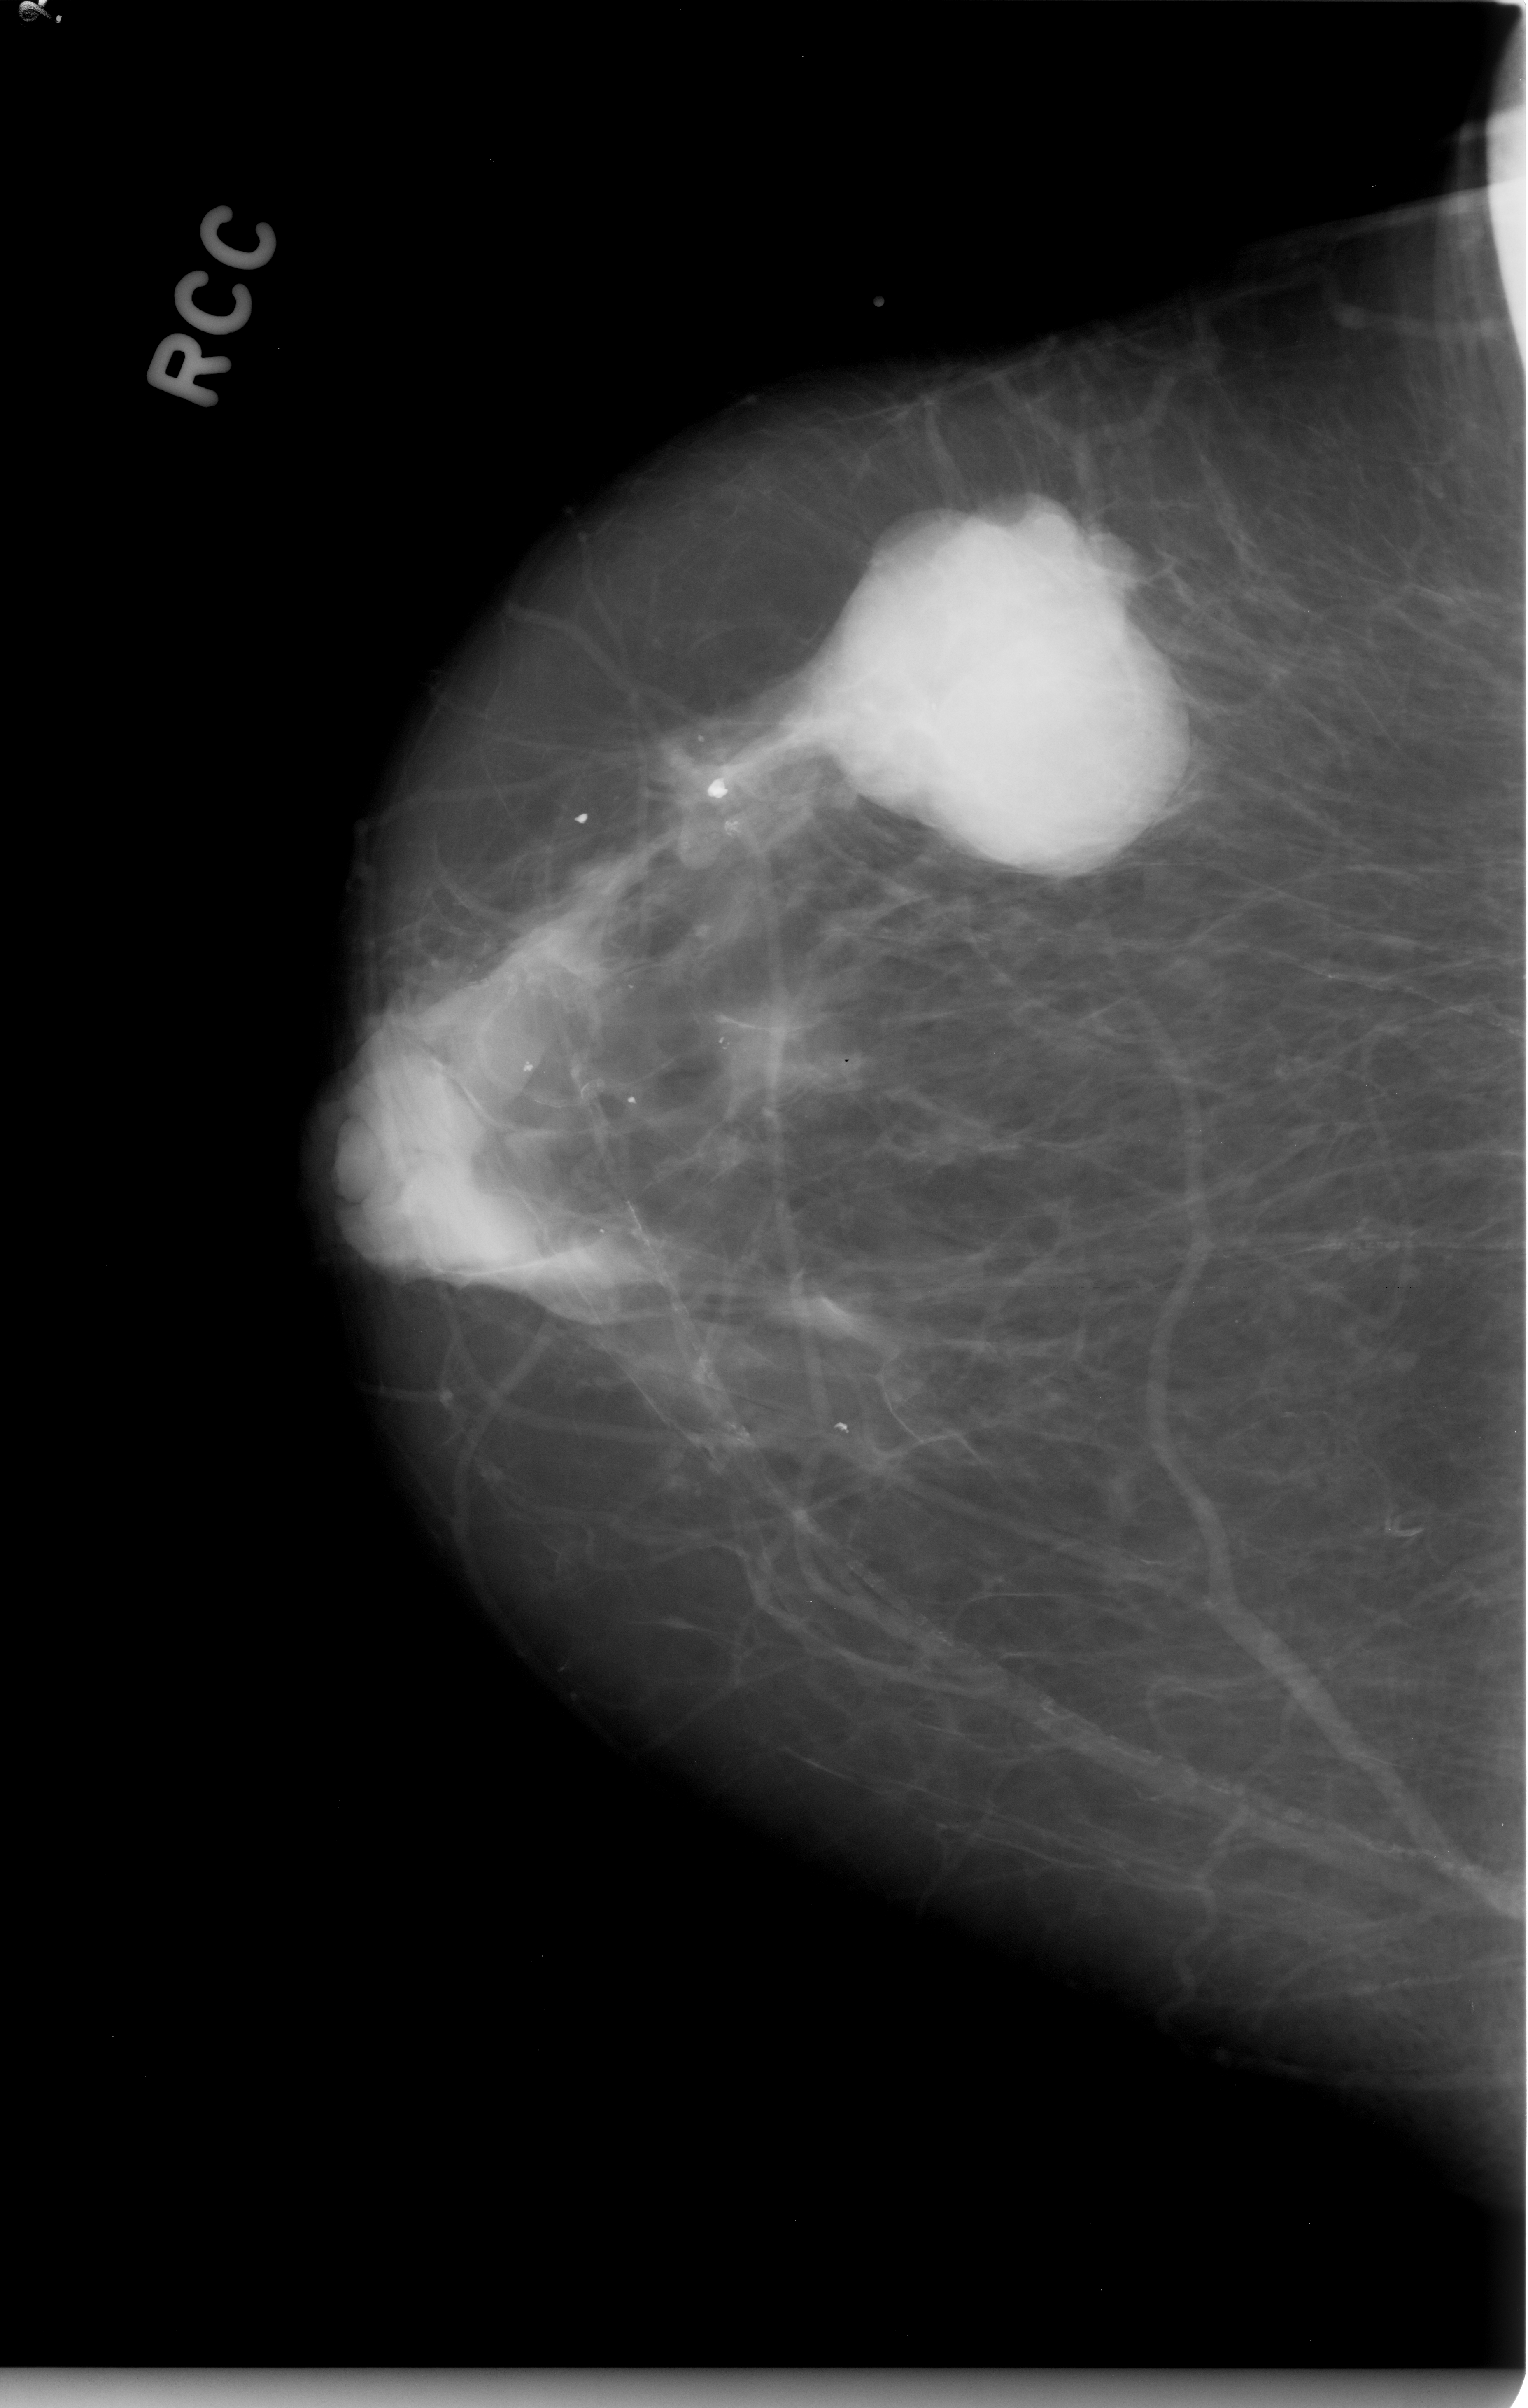
Digitized screen-film mammogram. Right breast. CC view. Breast composition: almost entirely fatty (BI-RADS density category 1 of 4). 1528 × 2408 image matrix.
Marked abnormalities (boxes around the expert regions of interest):
- mass, shape lobulated, margins circumscribed; BI-RADS assessment category 5; subtlety rating 5 on a 1 (subtle) to 5 (obvious) scale; pathology (as recorded): malignant: box from (x=801, y=494) to (x=1195, y=874) px